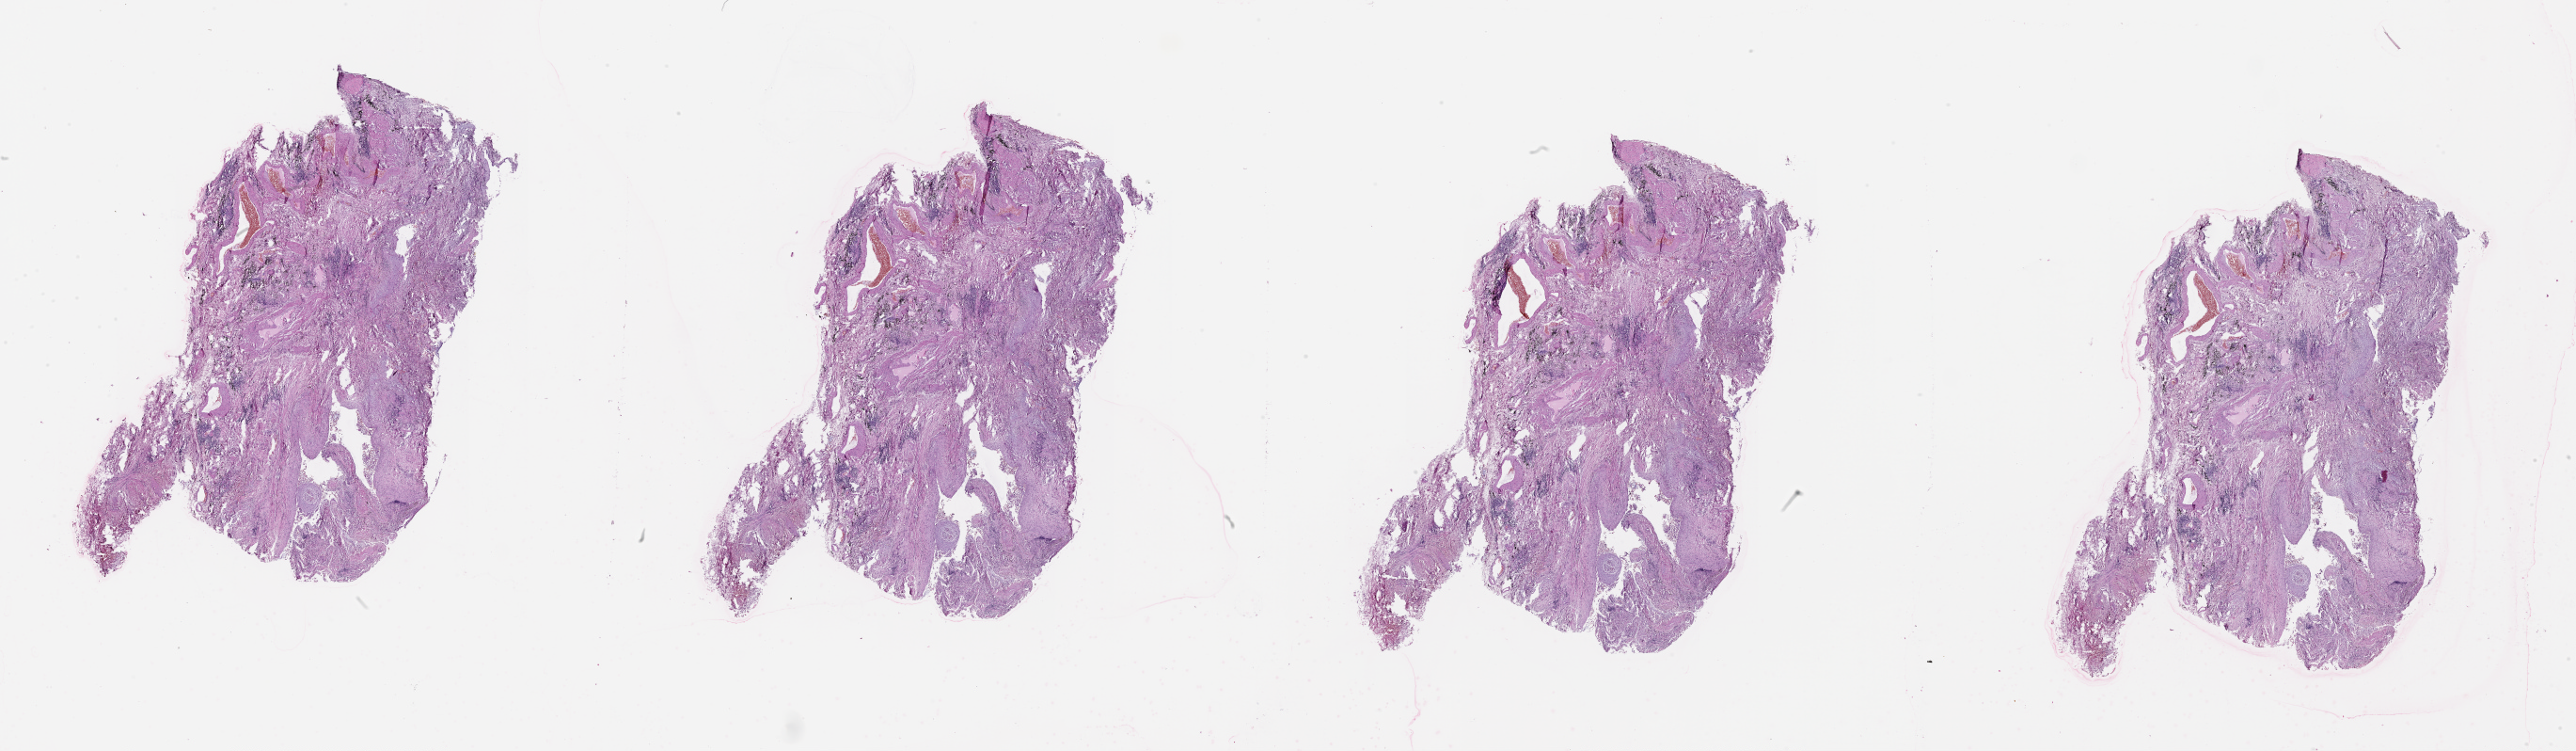
Whole-slide histology image, H&E, a low-resolution overview of the entire scanned area, about 44.1 x 12.8 mm. Lung, normal (non-tumour) tissue. Patient: male, age 72 years.
- this section: normal (non-tumour) tissue from the same patient
- patient diagnosis (cohort enrolment): squamous cell carcinoma (lung)